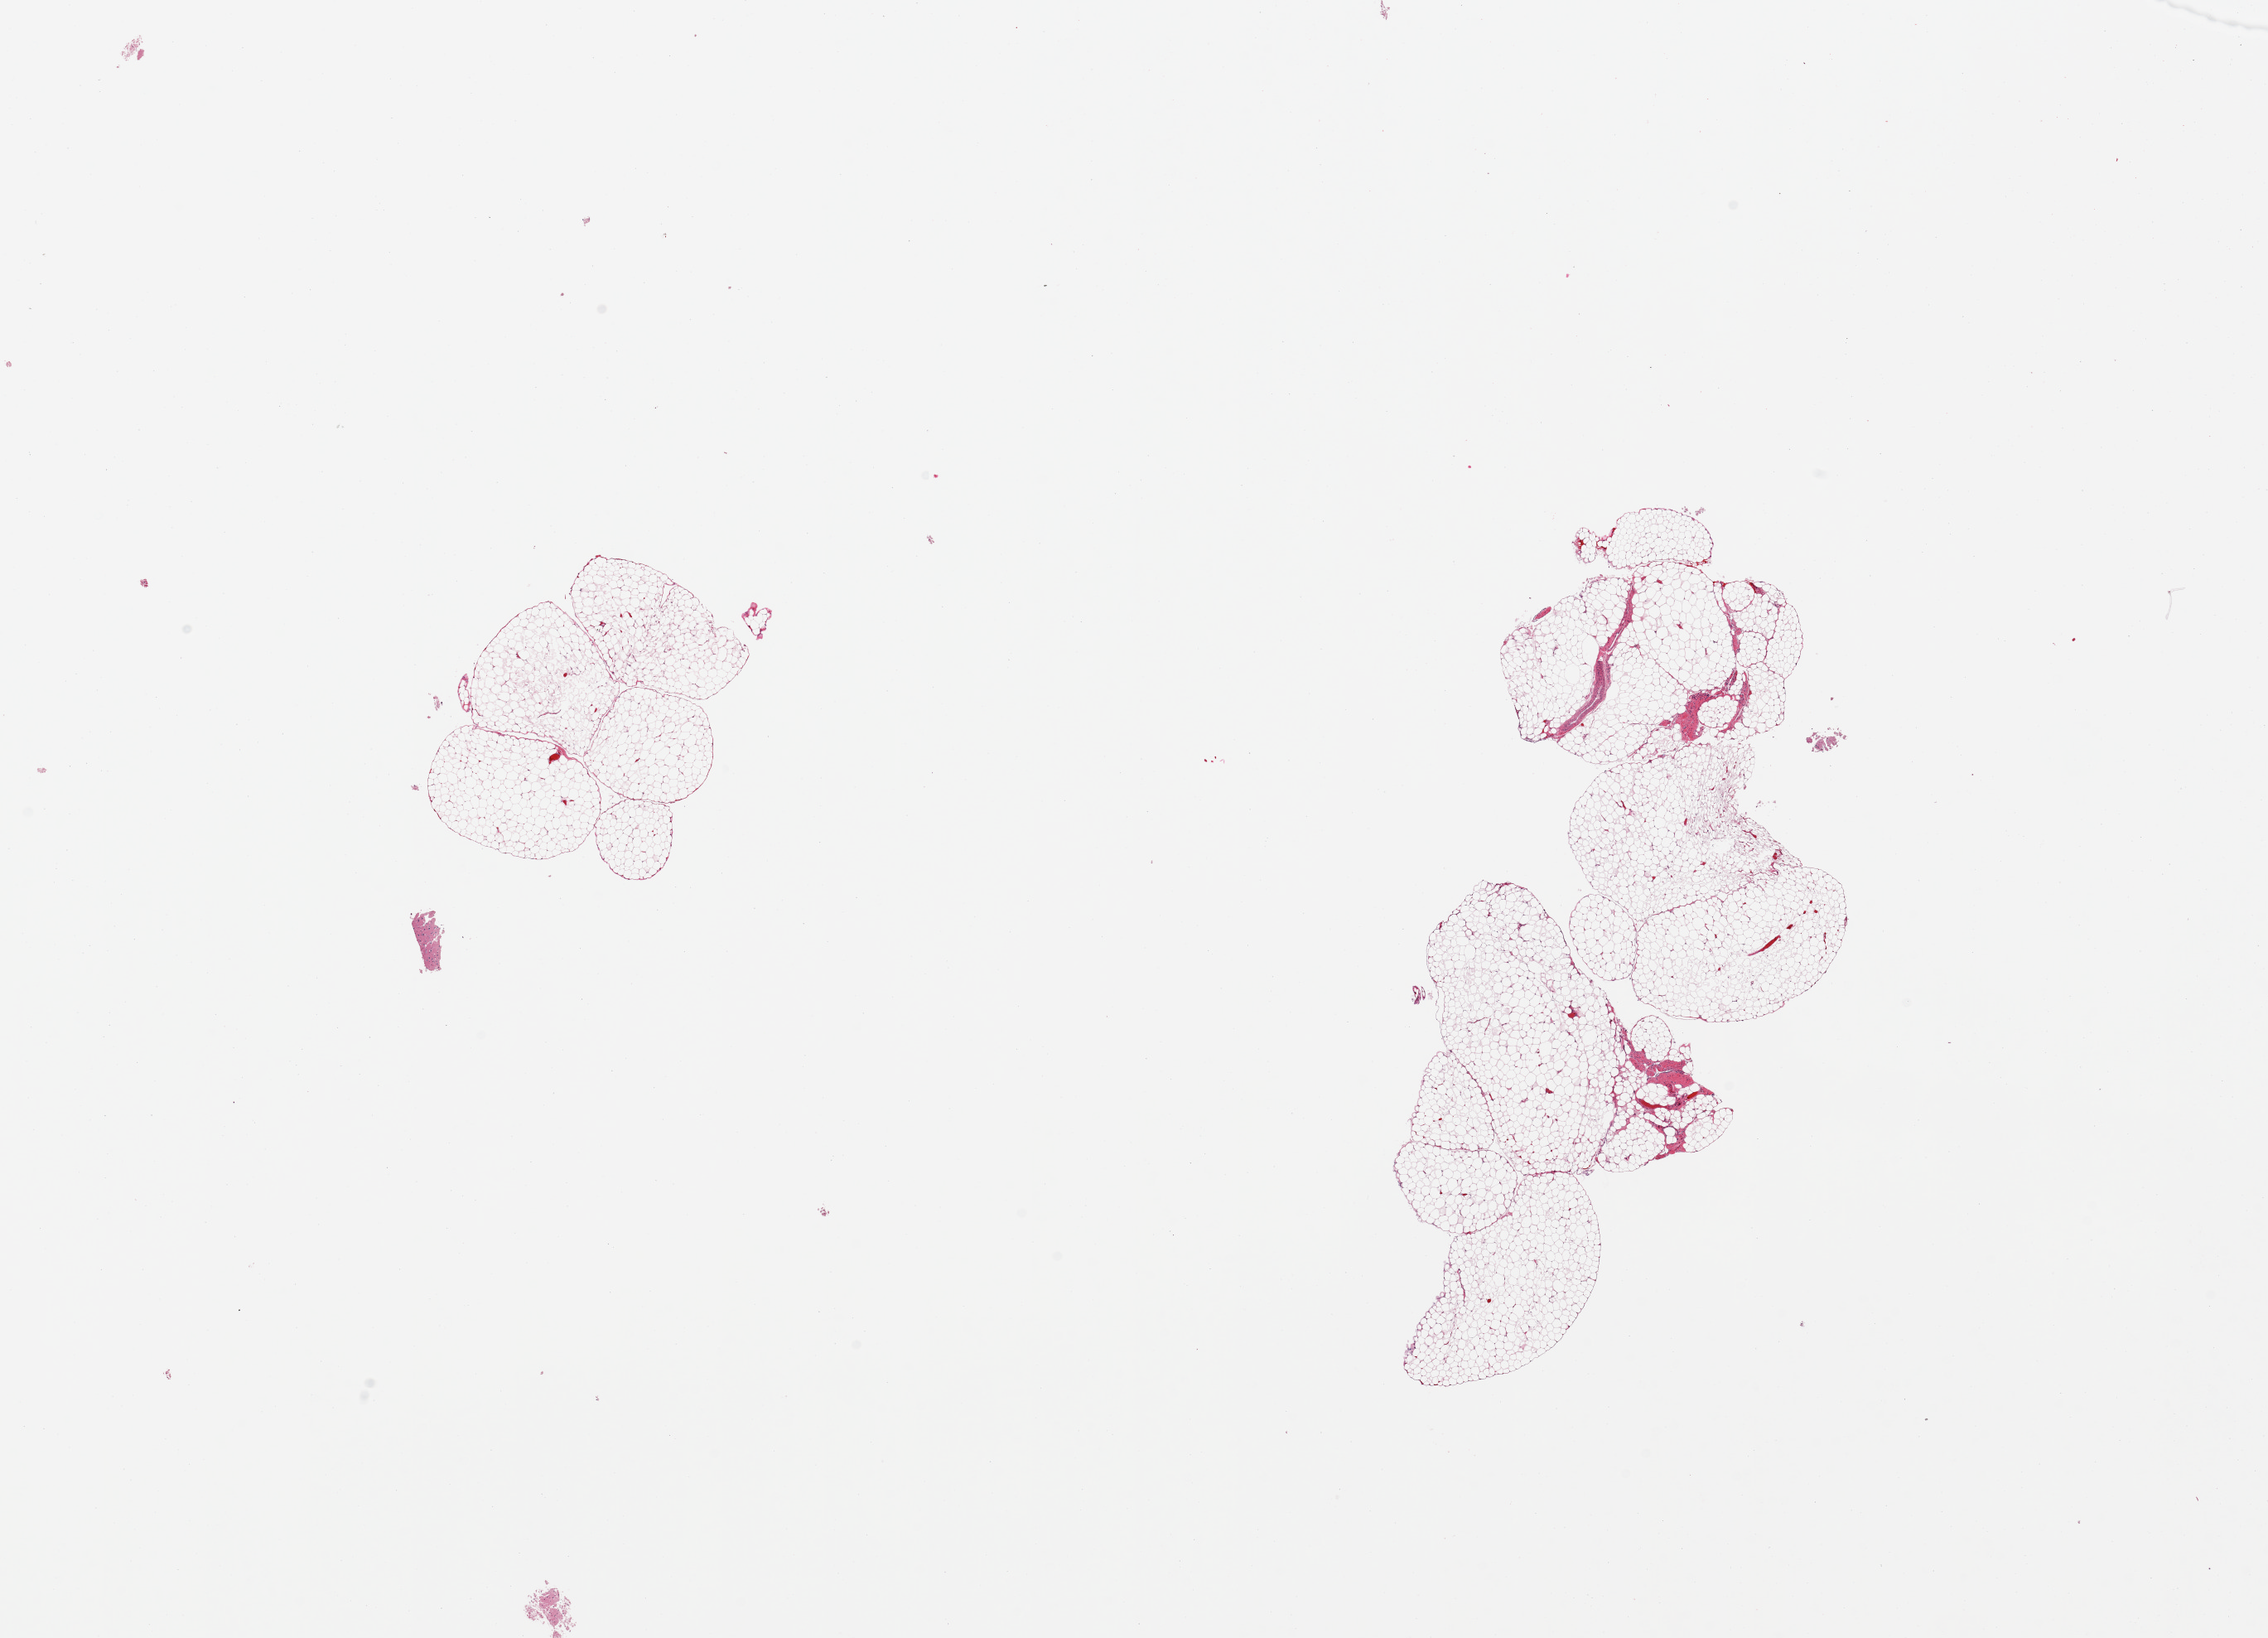
Digitized hematoxylin and eosin (H&E)-stained section, brightfield, shown as a low-resolution overview of the whole scanned area (about 21.7 x 15.6 mm, acquisition: 20x scan); PAXgene-fixed paraffin-embedded (PFPE) section; target tissue: omentum; tissue donor sample. Donor sex: male.
Reviewer comment on this tissue sample: 2 pieces.